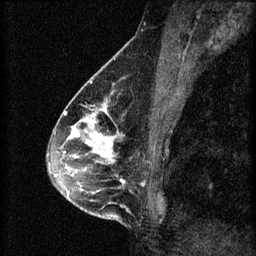
Breast MRI (dynamic contrast-enhanced), one sagittal slice; slice 30 of 60 in the series (ordered by position); 3 images stored at this slice position (order not interpretable as contrast timing); 1.5 T; TE 4.2 ms, TR 8.2 ms; 2 mm slice thickness; 256 × 256 image matrix, field of view 180 × 180 mm. Female patient, age 45 years.
Outlined on this slice (semi-automatically segmented with operator editing):
- analysis volume of interest (the breast-tissue region the enhancement analysis was run in; not a lesion): bounding box [x1, y1, x2, y2] px = [54, 104, 159, 217]
- tumour enhancement mask (voxels above the 70 % enhancement threshold inside the analysis volume of interest): [54, 104, 125, 197]